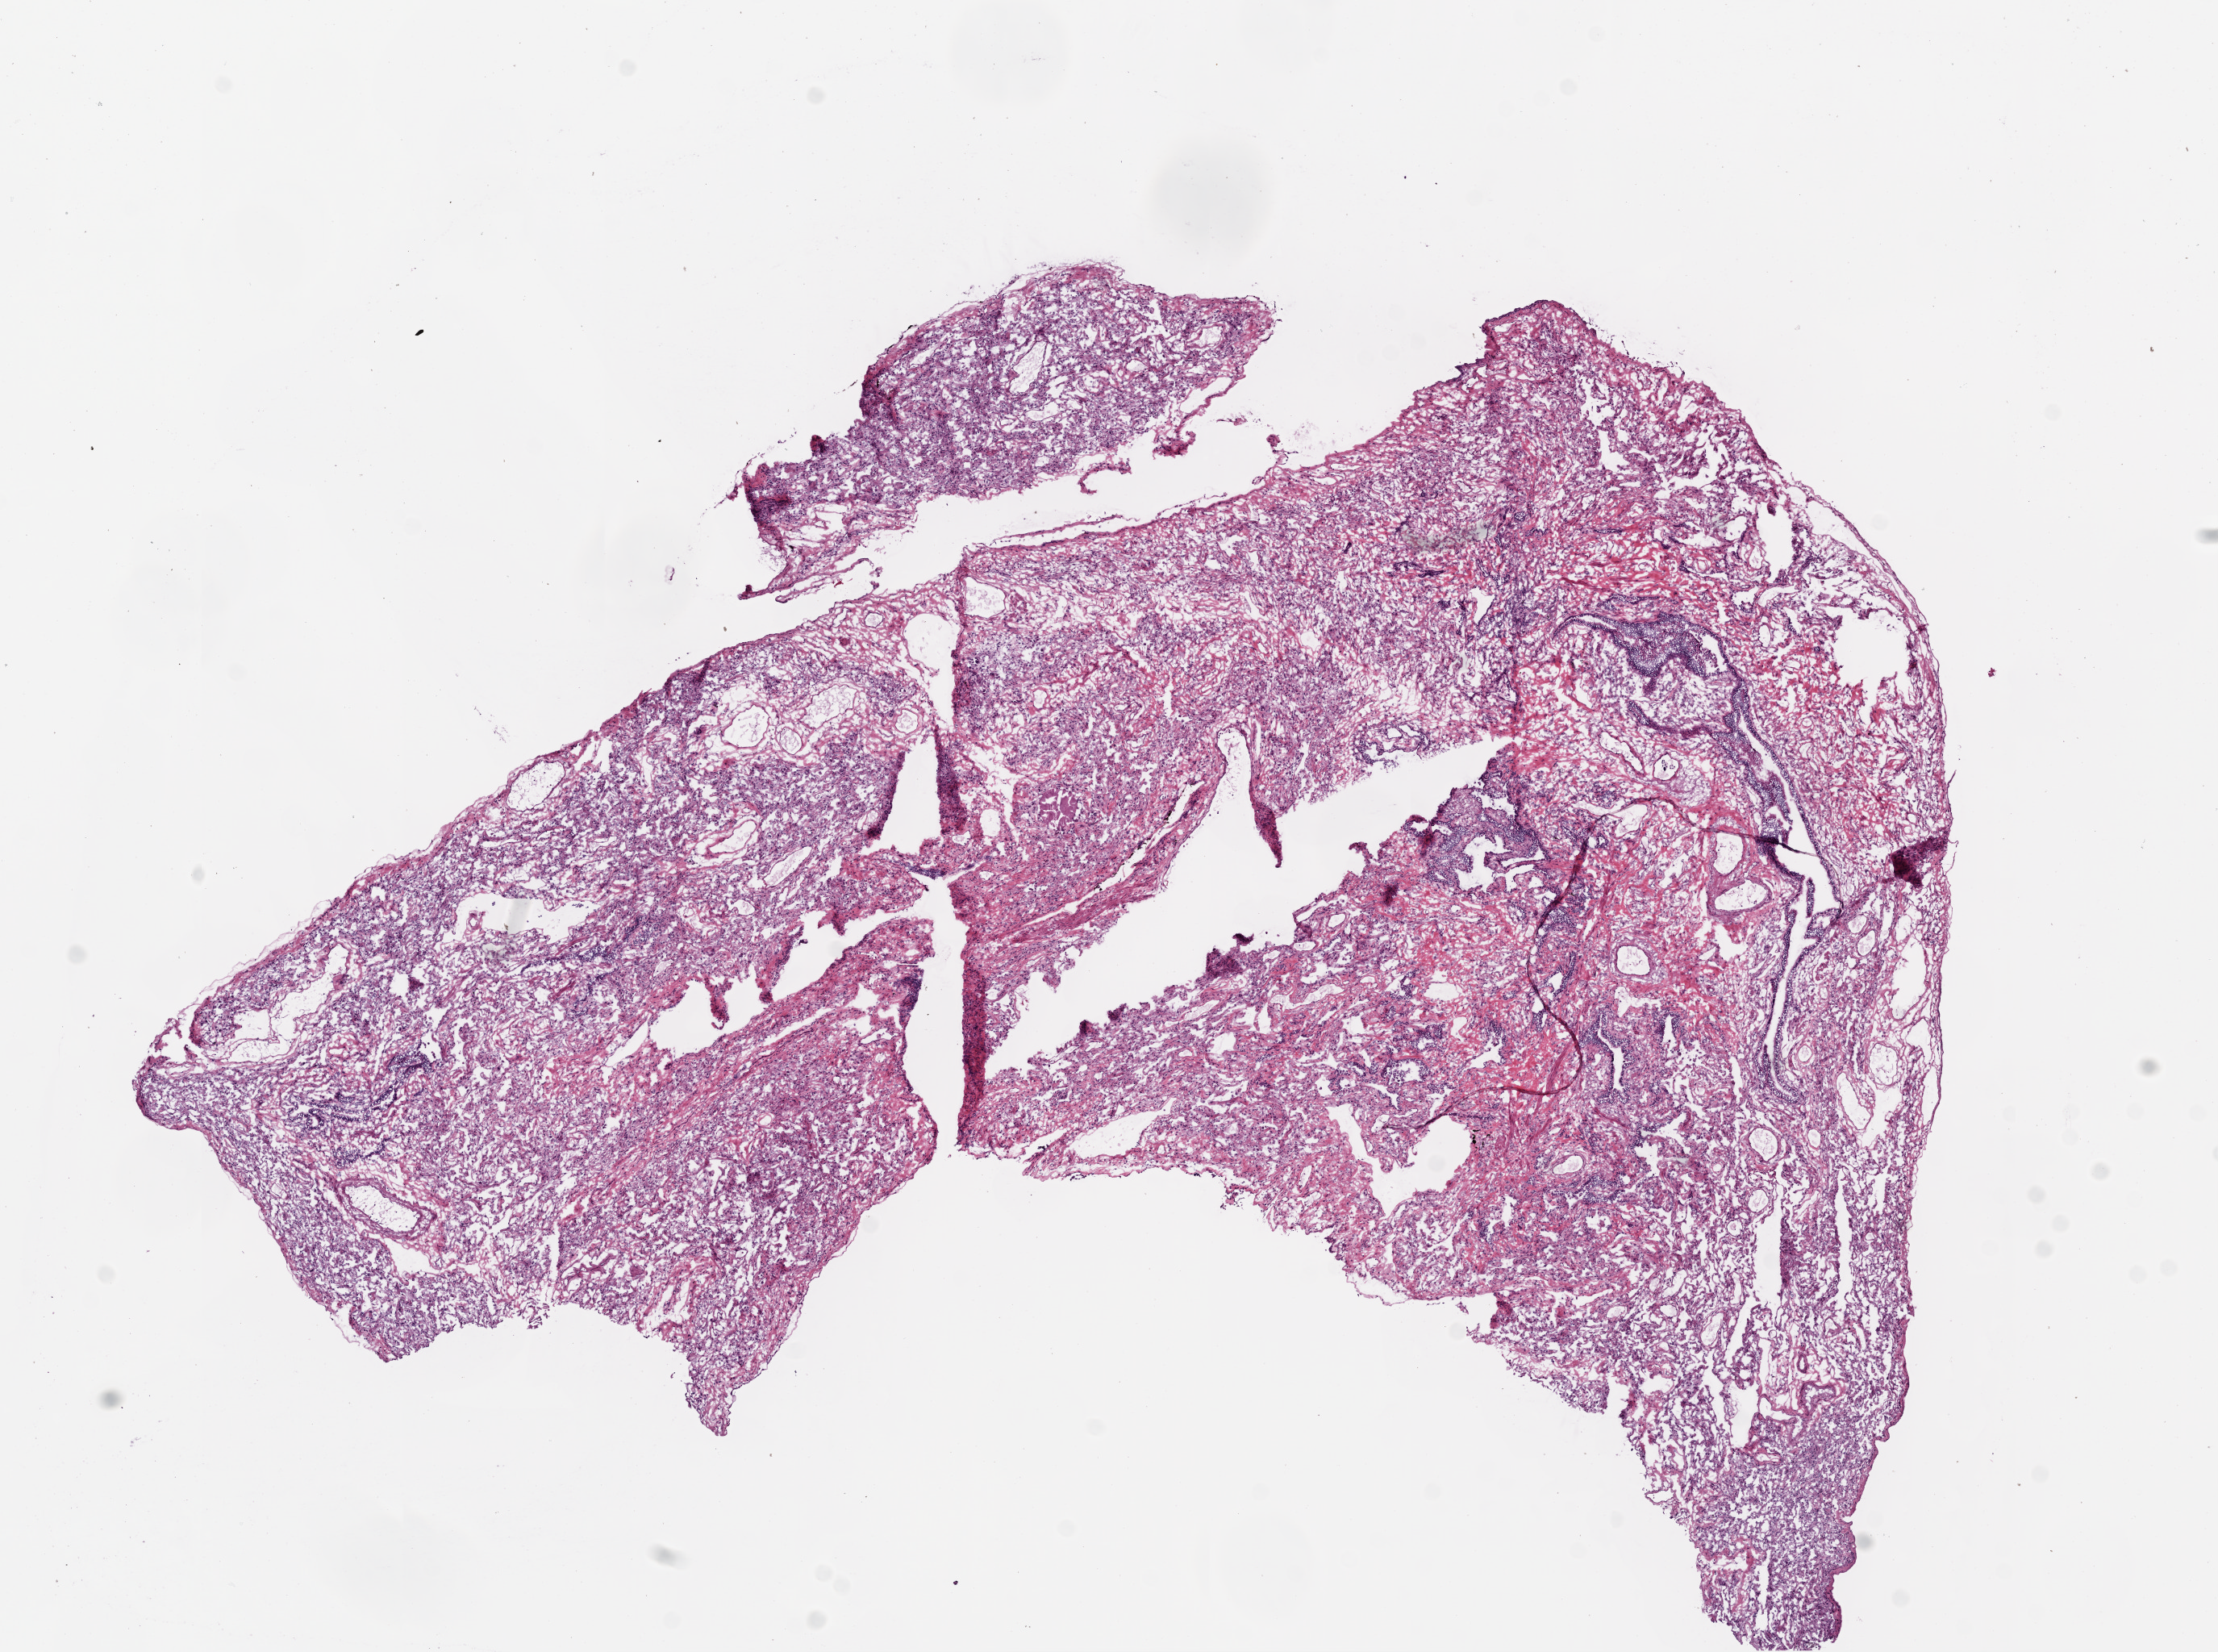
Whole-slide histology image, Hematoxylin and eosin (H&E) stained, low-resolution overview of the scanned area, about 11.0 x 8.2 mm, frozen section from the bottom of the tissue portion, lung, solid tissue normal (non-tumour tissue) sample. Female, age 68 years at initial diagnosis.
* this section: solid tissue normal (non-tumour) sample from the same patient
* patient diagnosis: Adenocarcinoma, NOS (upper lobe, lung)